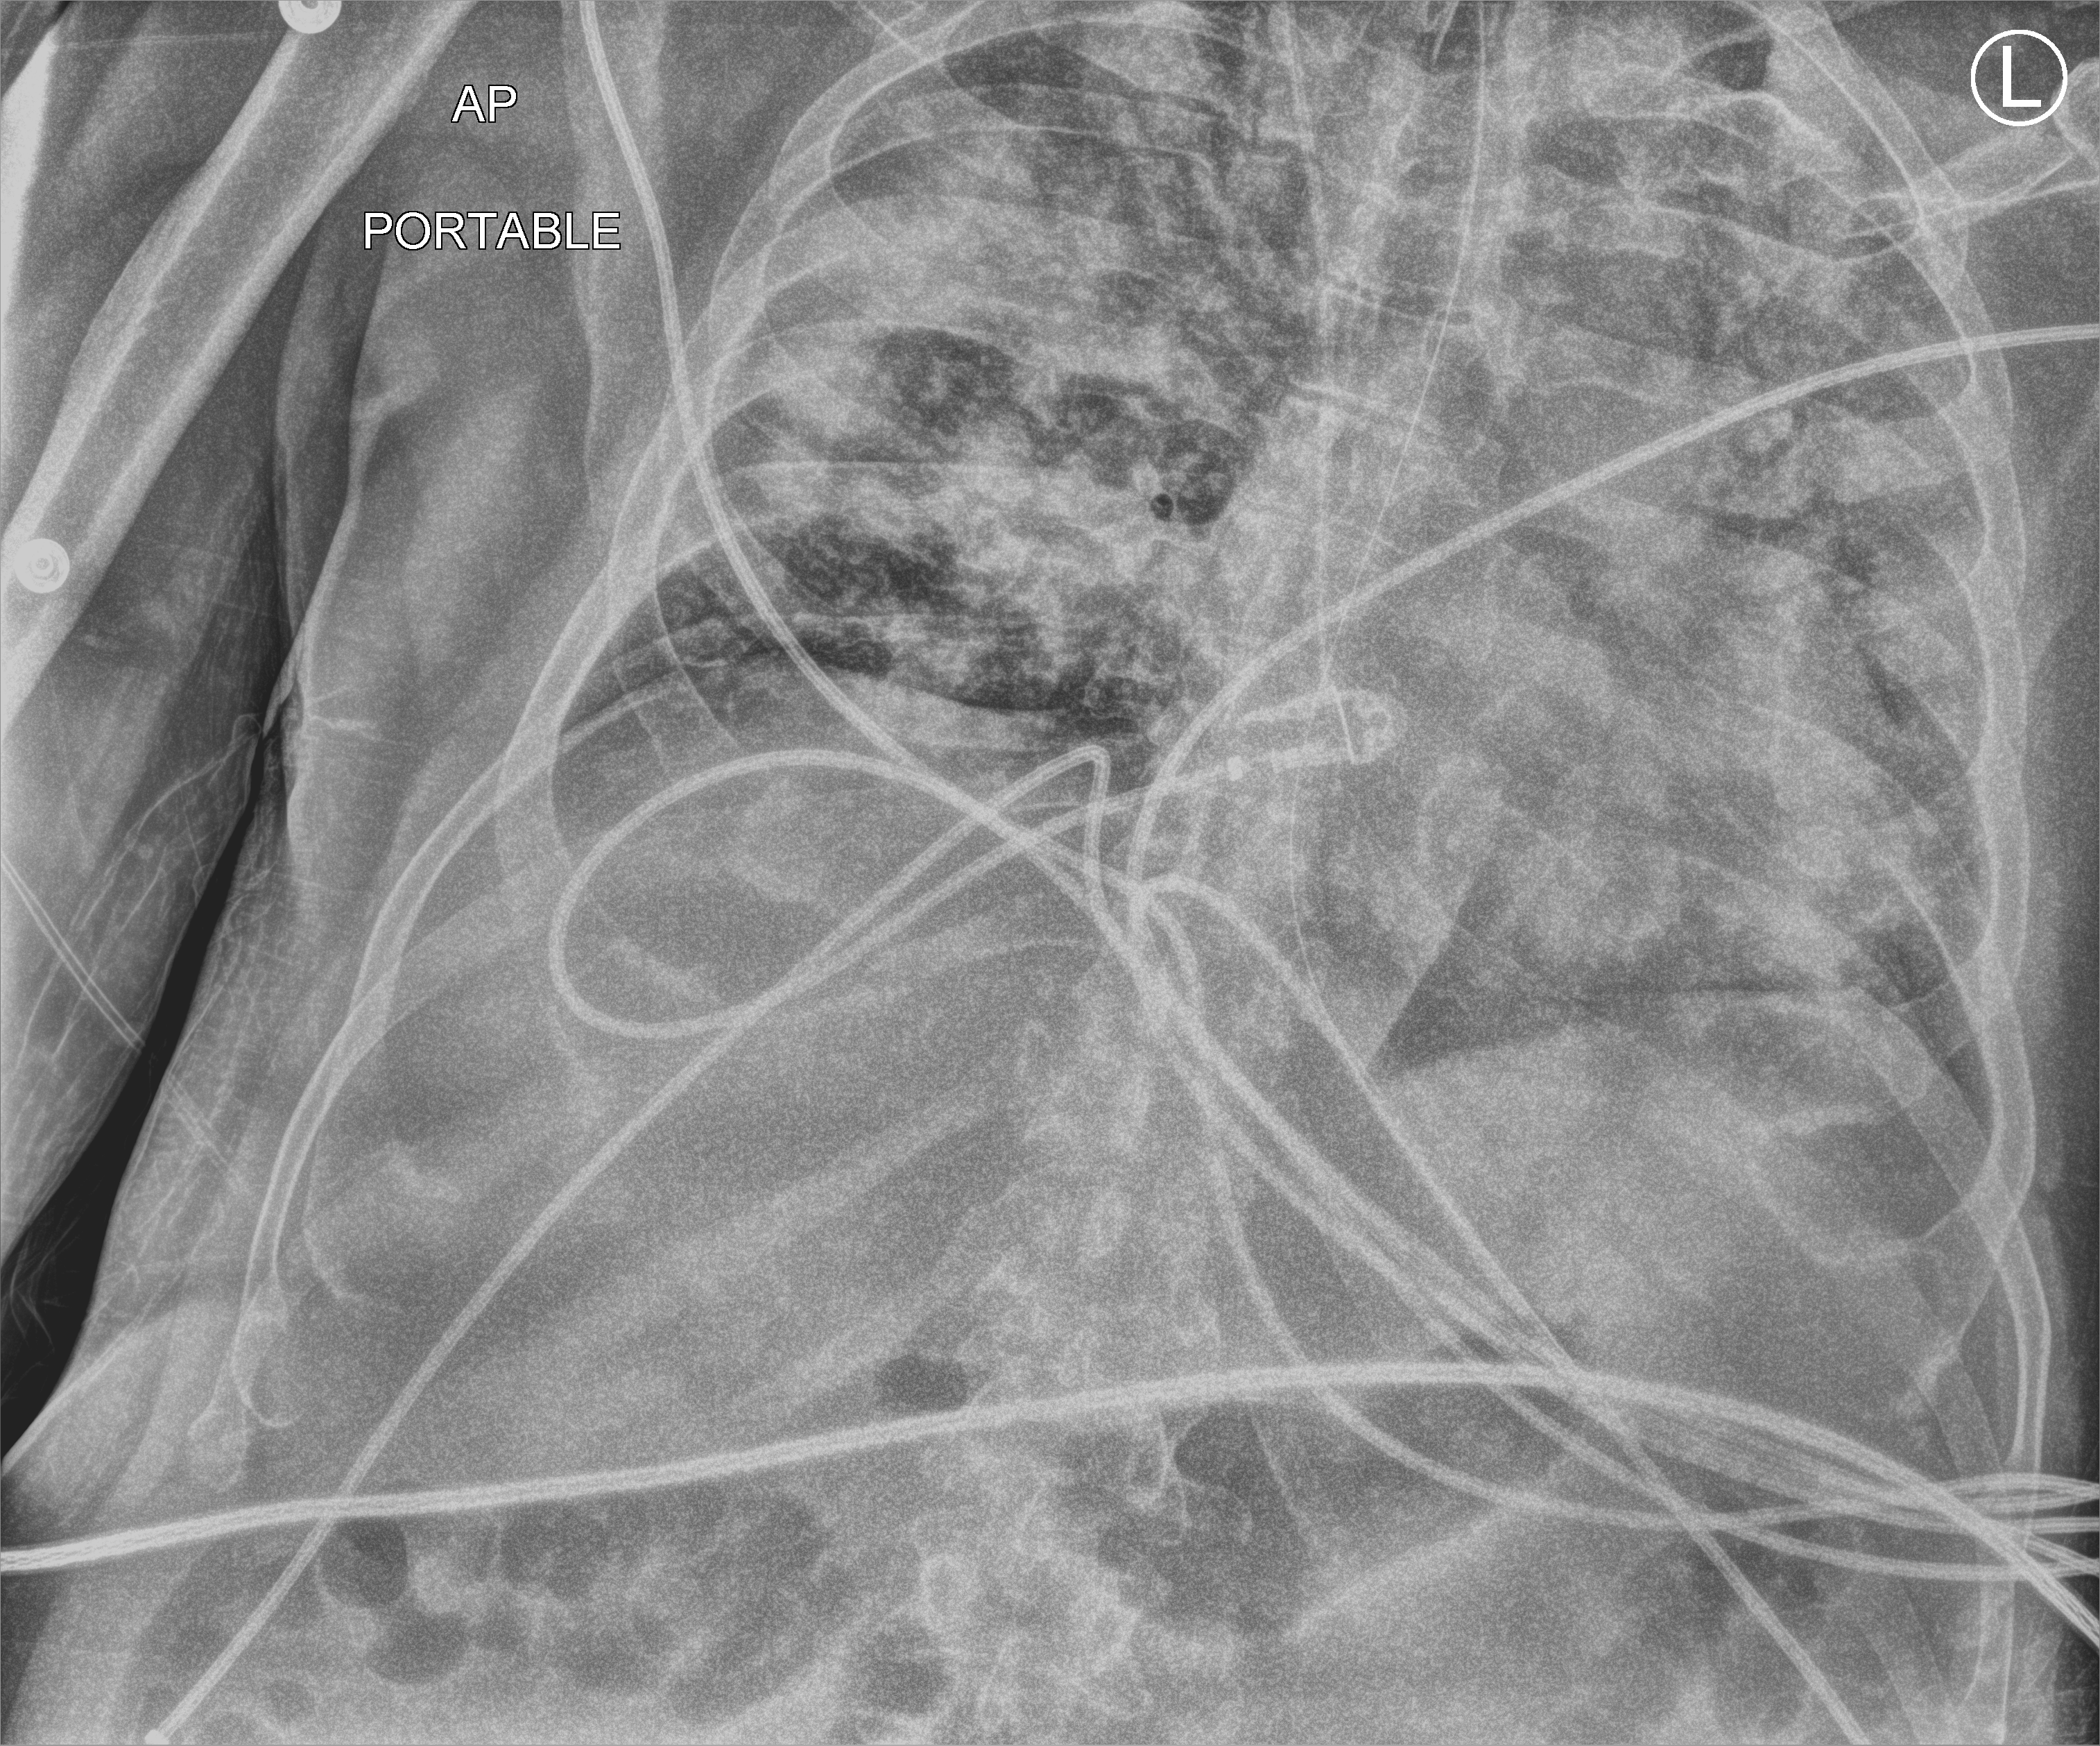
Bedside chest radiograph (computed radiography); anteroposterior (AP) projection. Patient hospitalised with COVID-19; male, aged 18–59 years.
From the hospital-stay record, not from the radiograph (when in the stay this image was taken is not recorded): admitted to intensive care during this hospital stay: yes; smoking status (admission record): never.